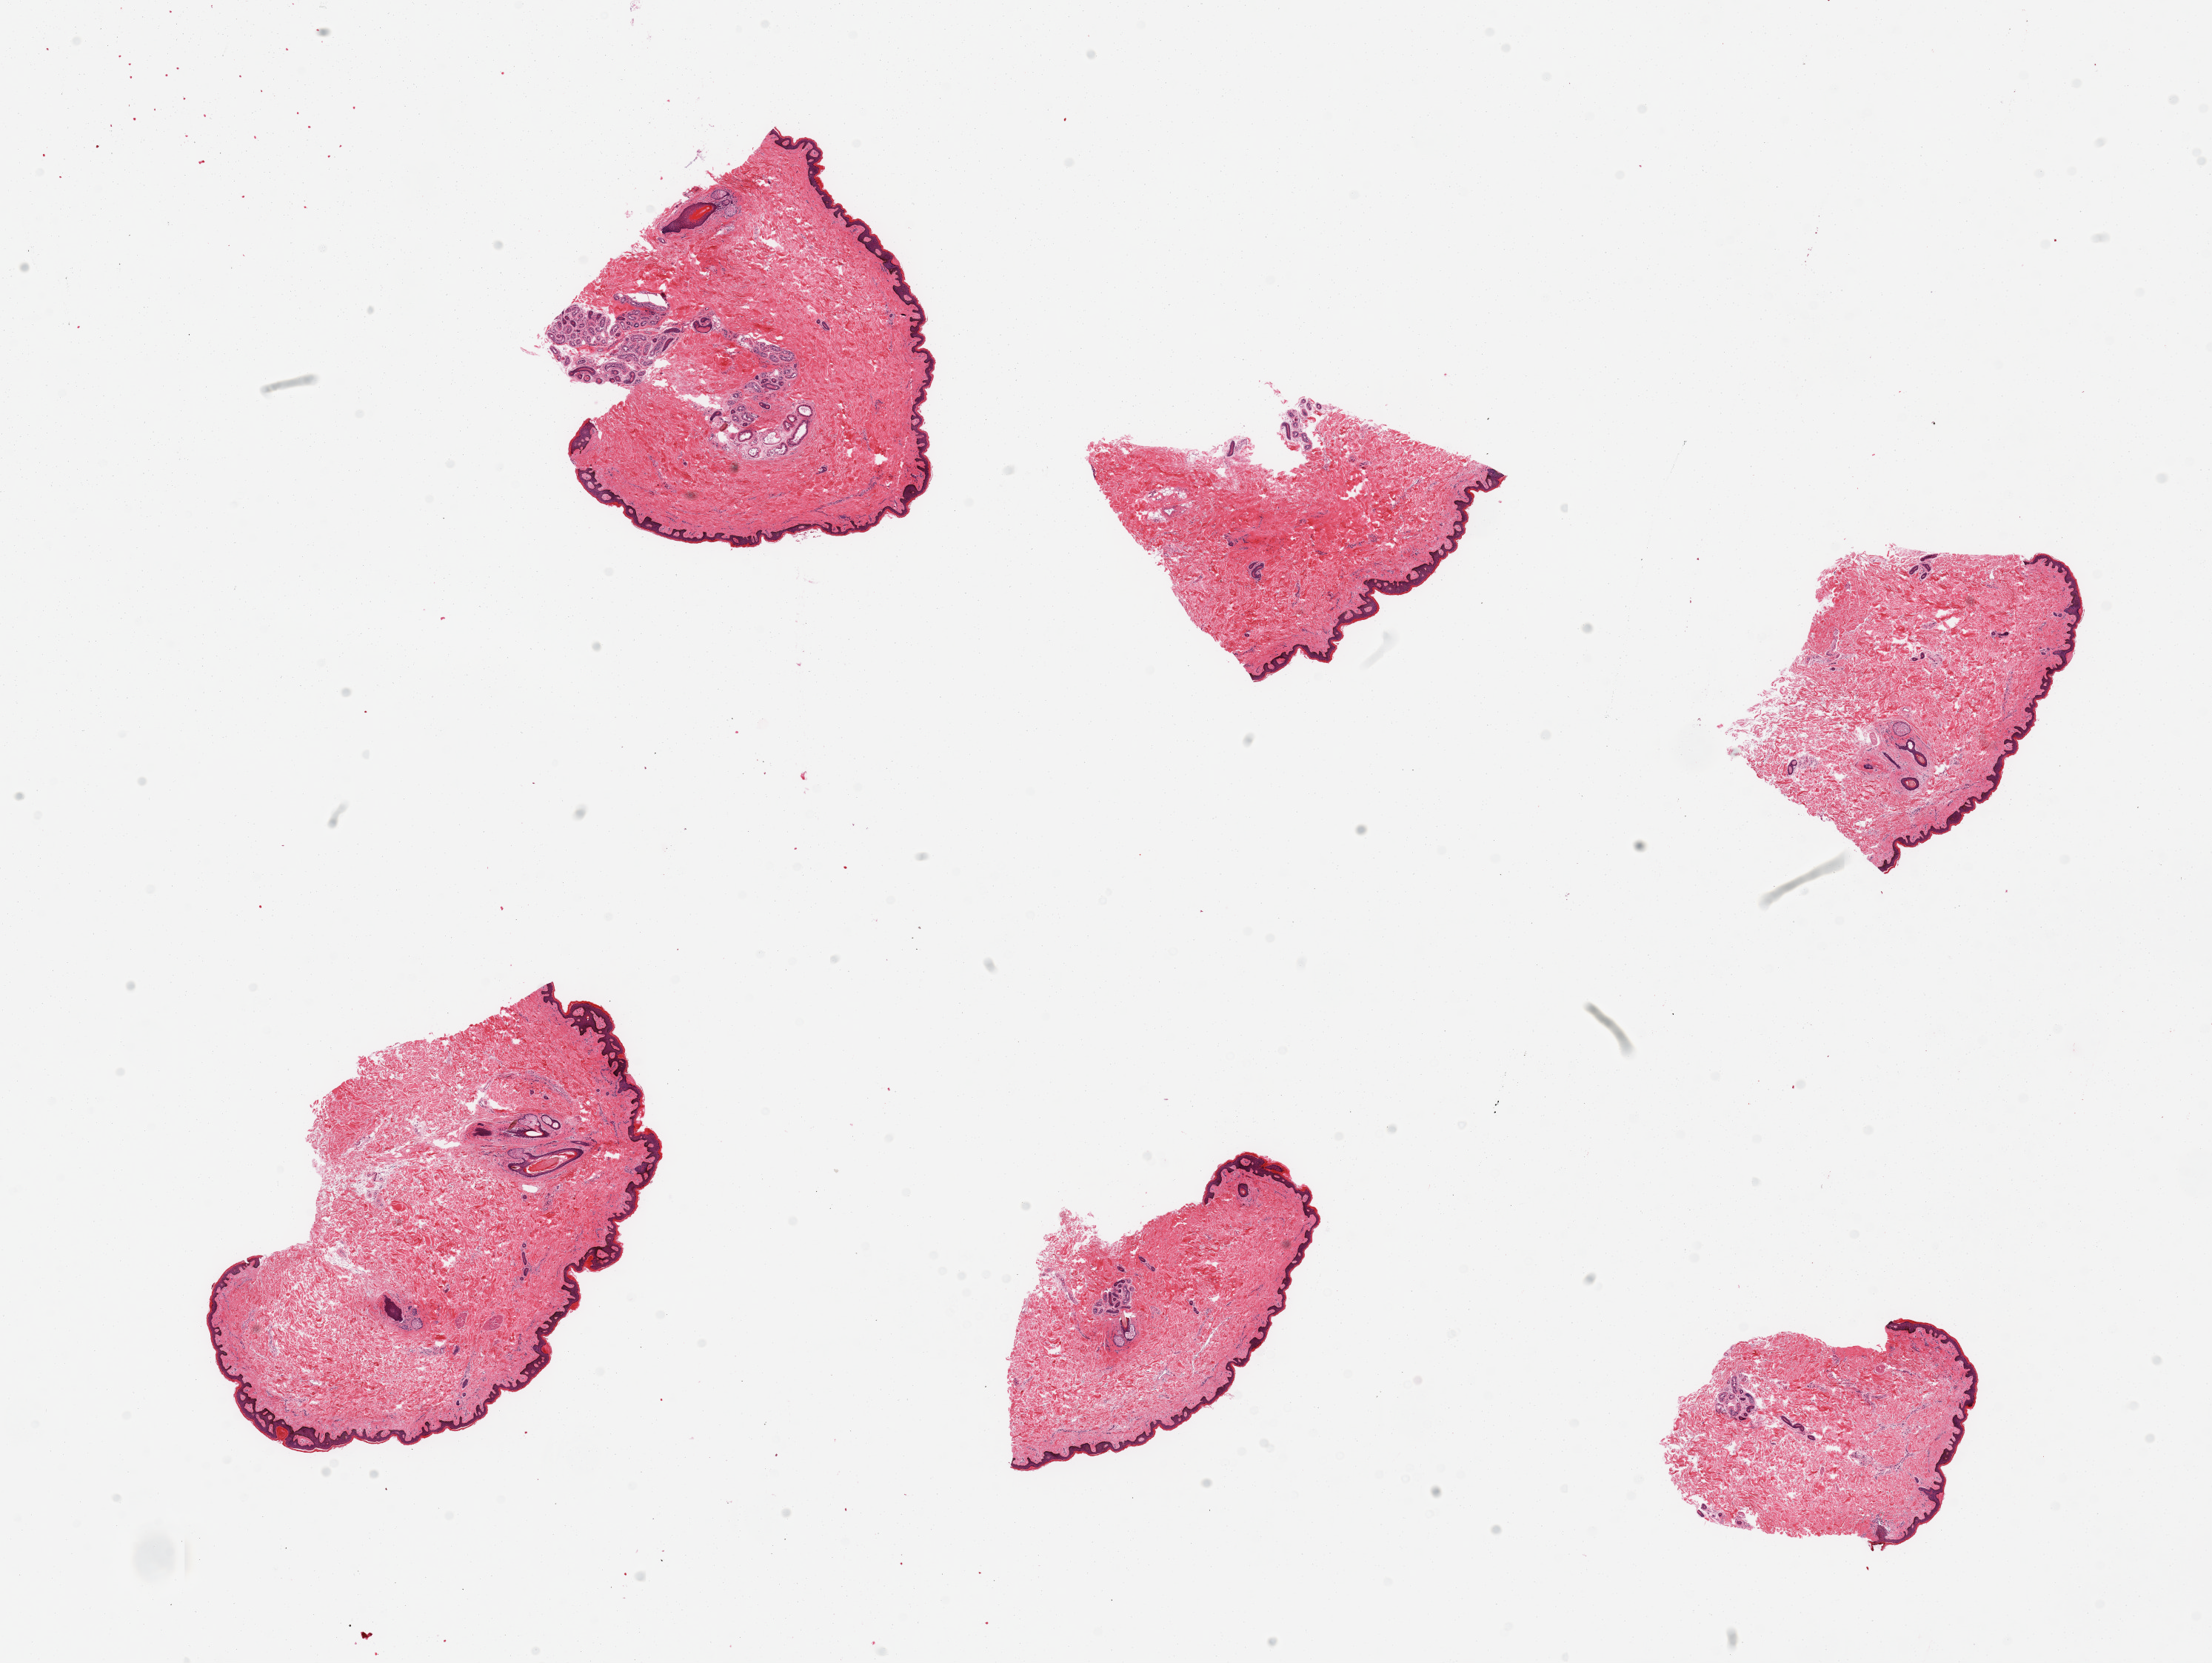
Haematoxylin and eosin whole-slide image — a low-resolution overview of the entire scanned area, about 23.6 x 17.8 mm (from a 20x scan). PAXgene-fixed paraffin-embedded (PFPE) section. Section of skin of suprapubic region (target tissue). Tissue donor sample. Donor sex: male.
Review note (as recorded): 6 pieces, well trimmed.